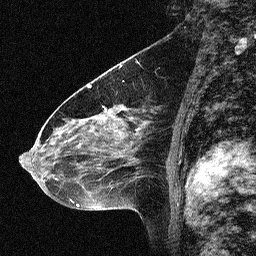
Breast MRI (dynamic contrast-enhanced), one sagittal slice; position 37 of 64 along the scan axis; dynamic contrast-enhanced study with each time point stored as its own series, time point 2 of 3 at this slice position (early post-contrast, ordered by acquisition time); 1.5 T; TE 4.5 ms, TR 11 ms; 2.06 mm slice thickness; 256 × 256 image matrix, field of view 200 × 200 mm. Female patient, age 46 years. From the clinical record (not read from this slice): setting: breast cancer imaged before/during neoadjuvant chemotherapy; receptor status: HER2-positive.
Structures marked on this image (semi-automatically segmented with operator editing):
- analysis volume of interest (the breast-tissue region the enhancement analysis was run in; not a lesion): bounding box [x1, y1, x2, y2] px = [42, 80, 150, 180]
- tumour enhancement mask (voxels above the 90 % enhancement threshold inside the analysis volume of interest): [92, 106, 141, 164]